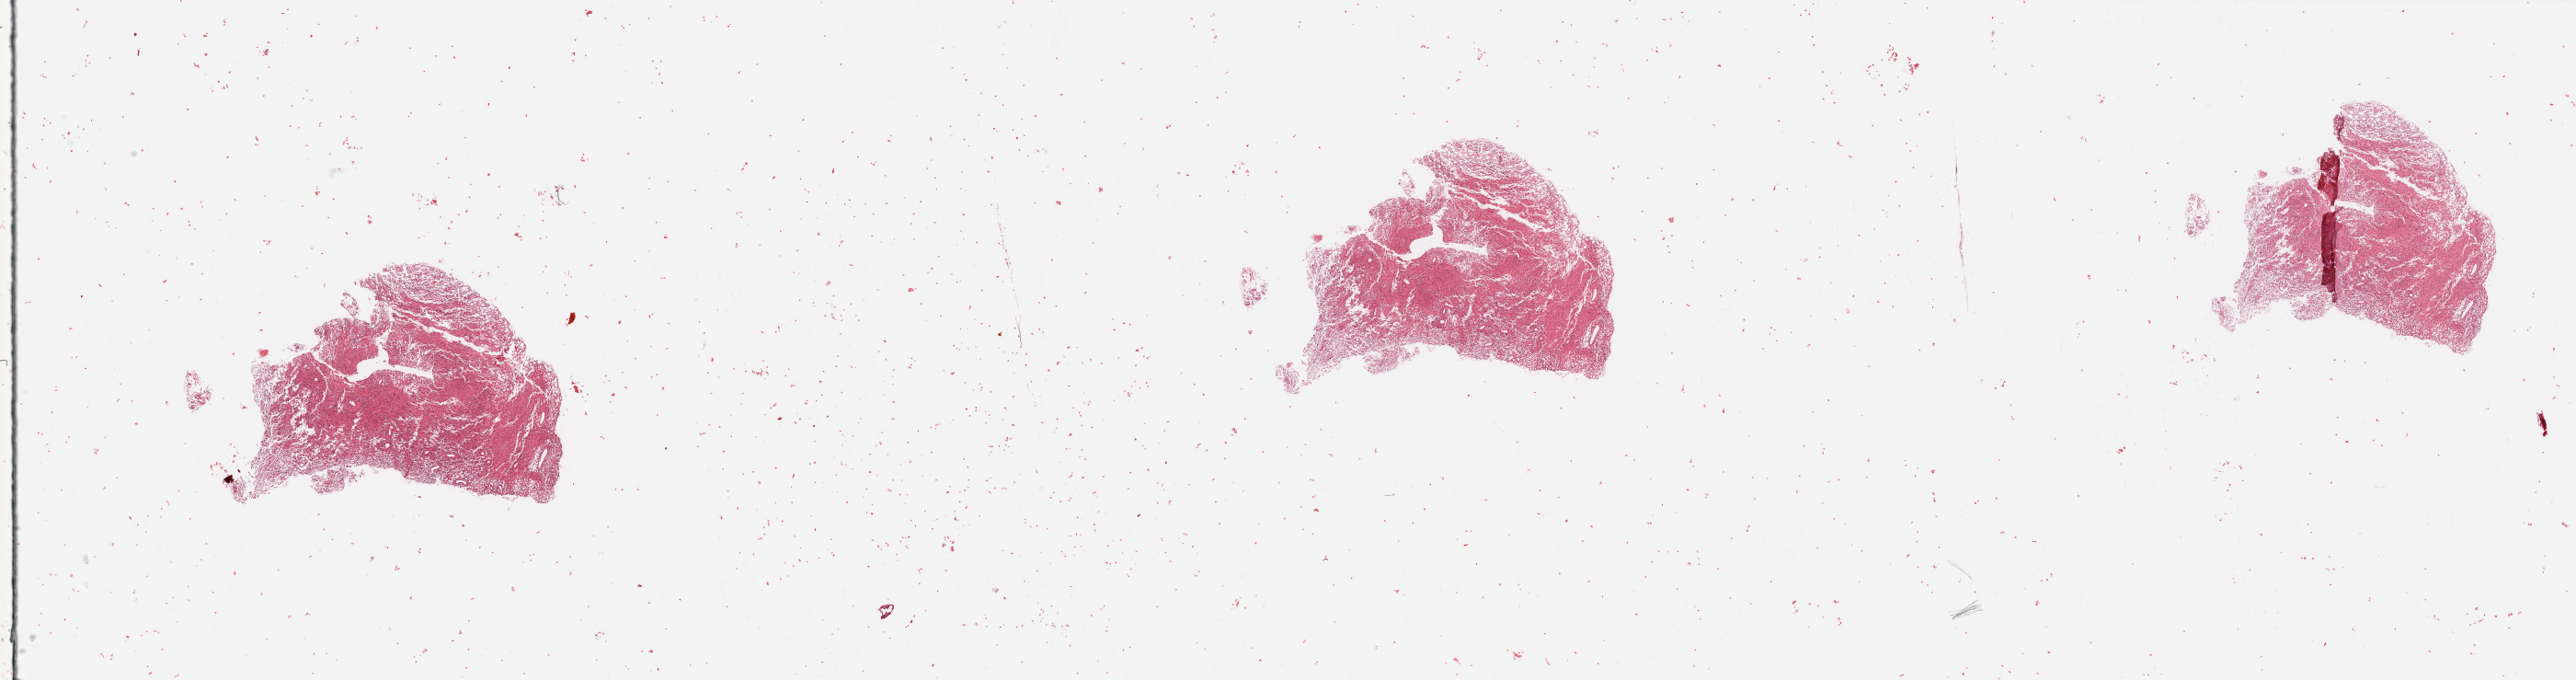
Digitized H&E tissue section (whole slide) — low-resolution overview of the scanned area, about 44.3 x 11.7 mm (slide scanned at 20x); tumour tissue sample, sampled site: brain. 78-year-old male patient. Pathologist review of this section (percent, as recorded): tumour nuclei 85%, necrosis 7%.
Diagnosis: Glioblastoma. Primary tumour site (as recorded): temporal lobe.